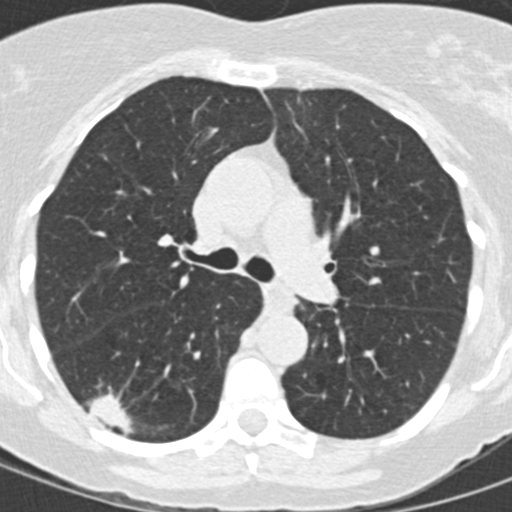
Low-dose screening chest CT, one axial slice. Position 91 of 146 along the scan axis. Reconstruction kernel B30f. 120 kVp. Lung window (W 1500 / L -600 HU). 2 mm slice thickness. 512 × 512 image matrix, field of view 270 × 270 mm.
Structures marked on this image (expert manual segmentation):
- lesion 1 (tumor, lower lobe of right lung): bounding box (x1, y1, x2, y2) in pixels: (88, 395, 134, 435)